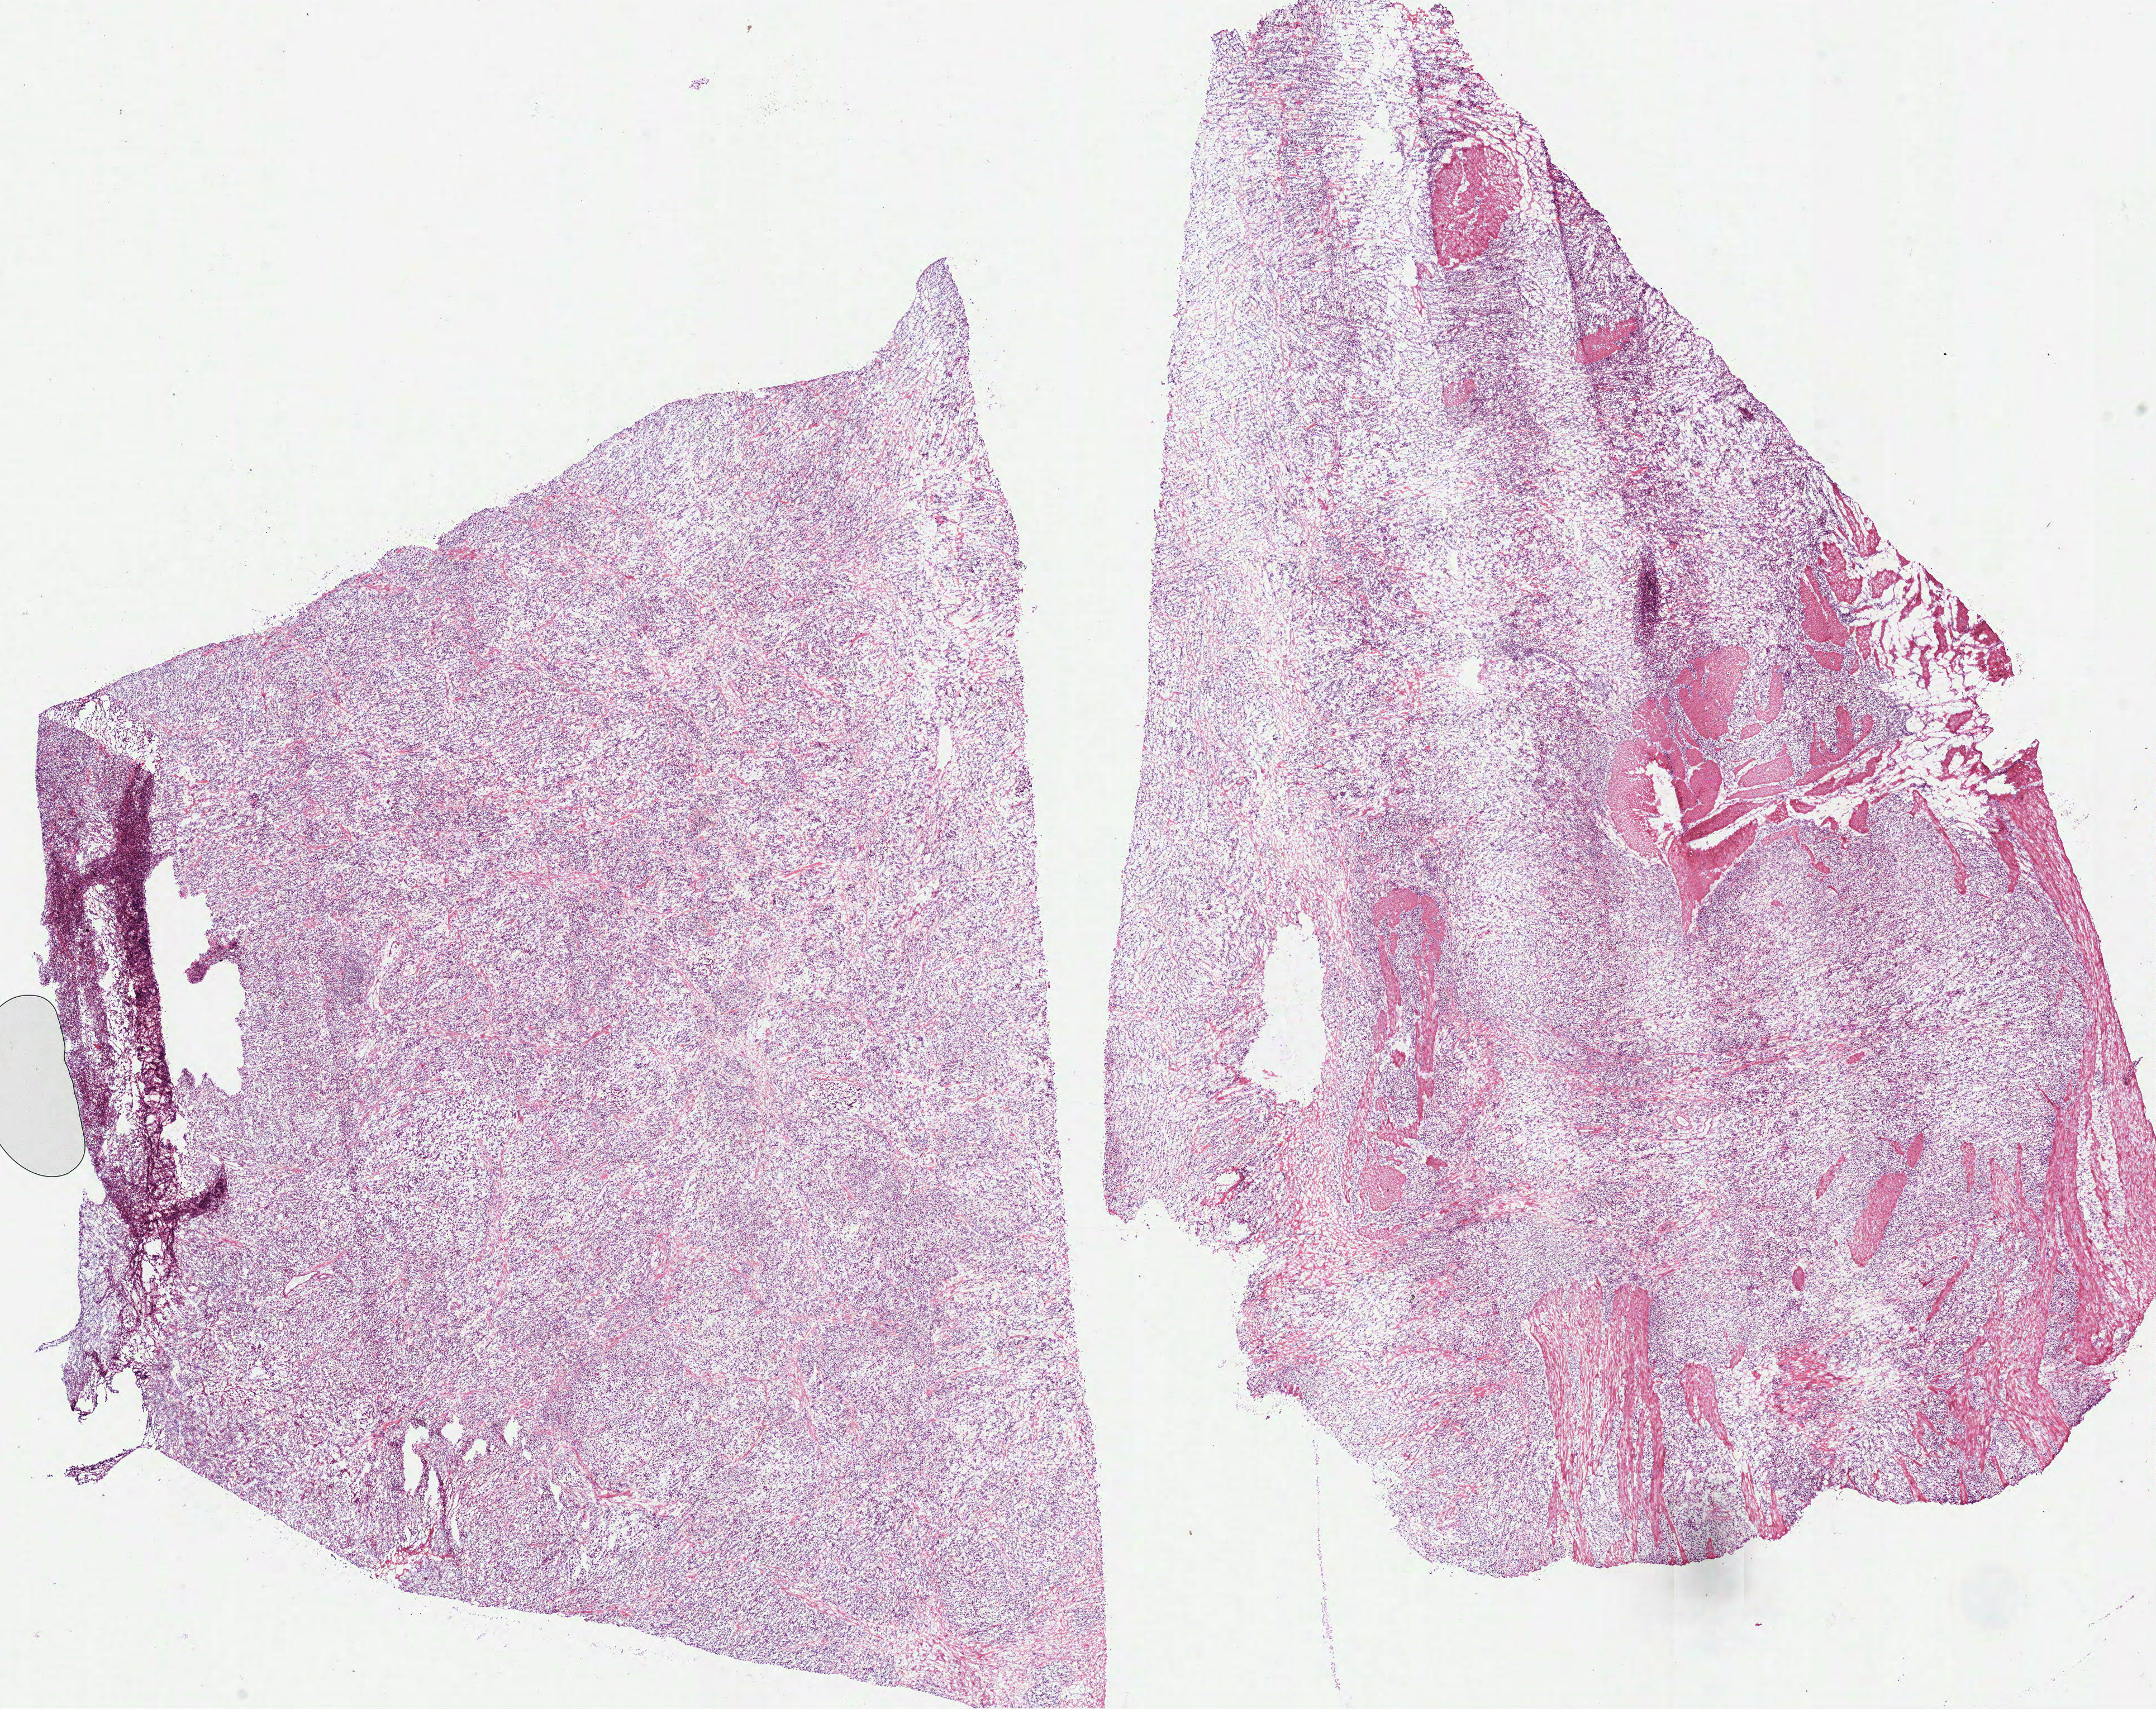
Digitized Hematoxylin and eosin (H&E) stained tissue section (whole slide), a low-resolution overview of the entire scanned area, about 15.6 x 12.3 mm (slide scanned at 40x), frozen section, primary tumour sample from the stomach. Male patient; age at initial diagnosis 41 years. Histologic grade: G3 (poorly differentiated). Slide review estimates, as recorded: tumour cells 90%, tumour nuclei 85%, normal cells 0%, stromal cells 10%, necrosis 0%.
• AJCC pathologic stage: II
• histologic diagnosis: Carcinoma, diffuse type (gastric antrum)